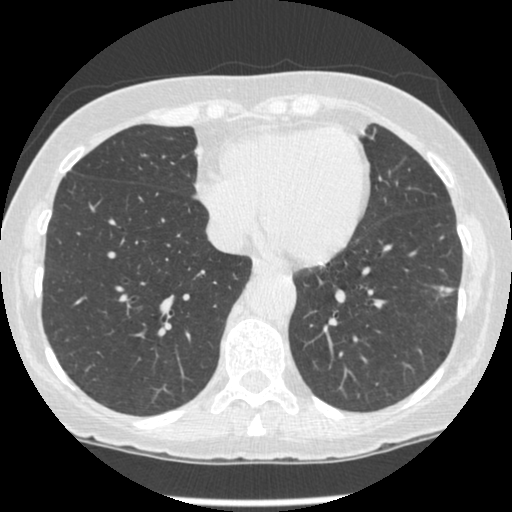
Low-dose screening chest CT, one axial slice. Position 82 of 247 along the scan axis. Lung window (W 1500 / L -600 HU). 1.25 mm slice thickness. 512 × 512 image matrix, field of view 303 × 303 mm.
Annotated regions visible in this slice (manually delineated by an expert):
- lesion 1 (tumor, lower lobe of left lung): box from (x=439, y=286) to (x=453, y=296) px